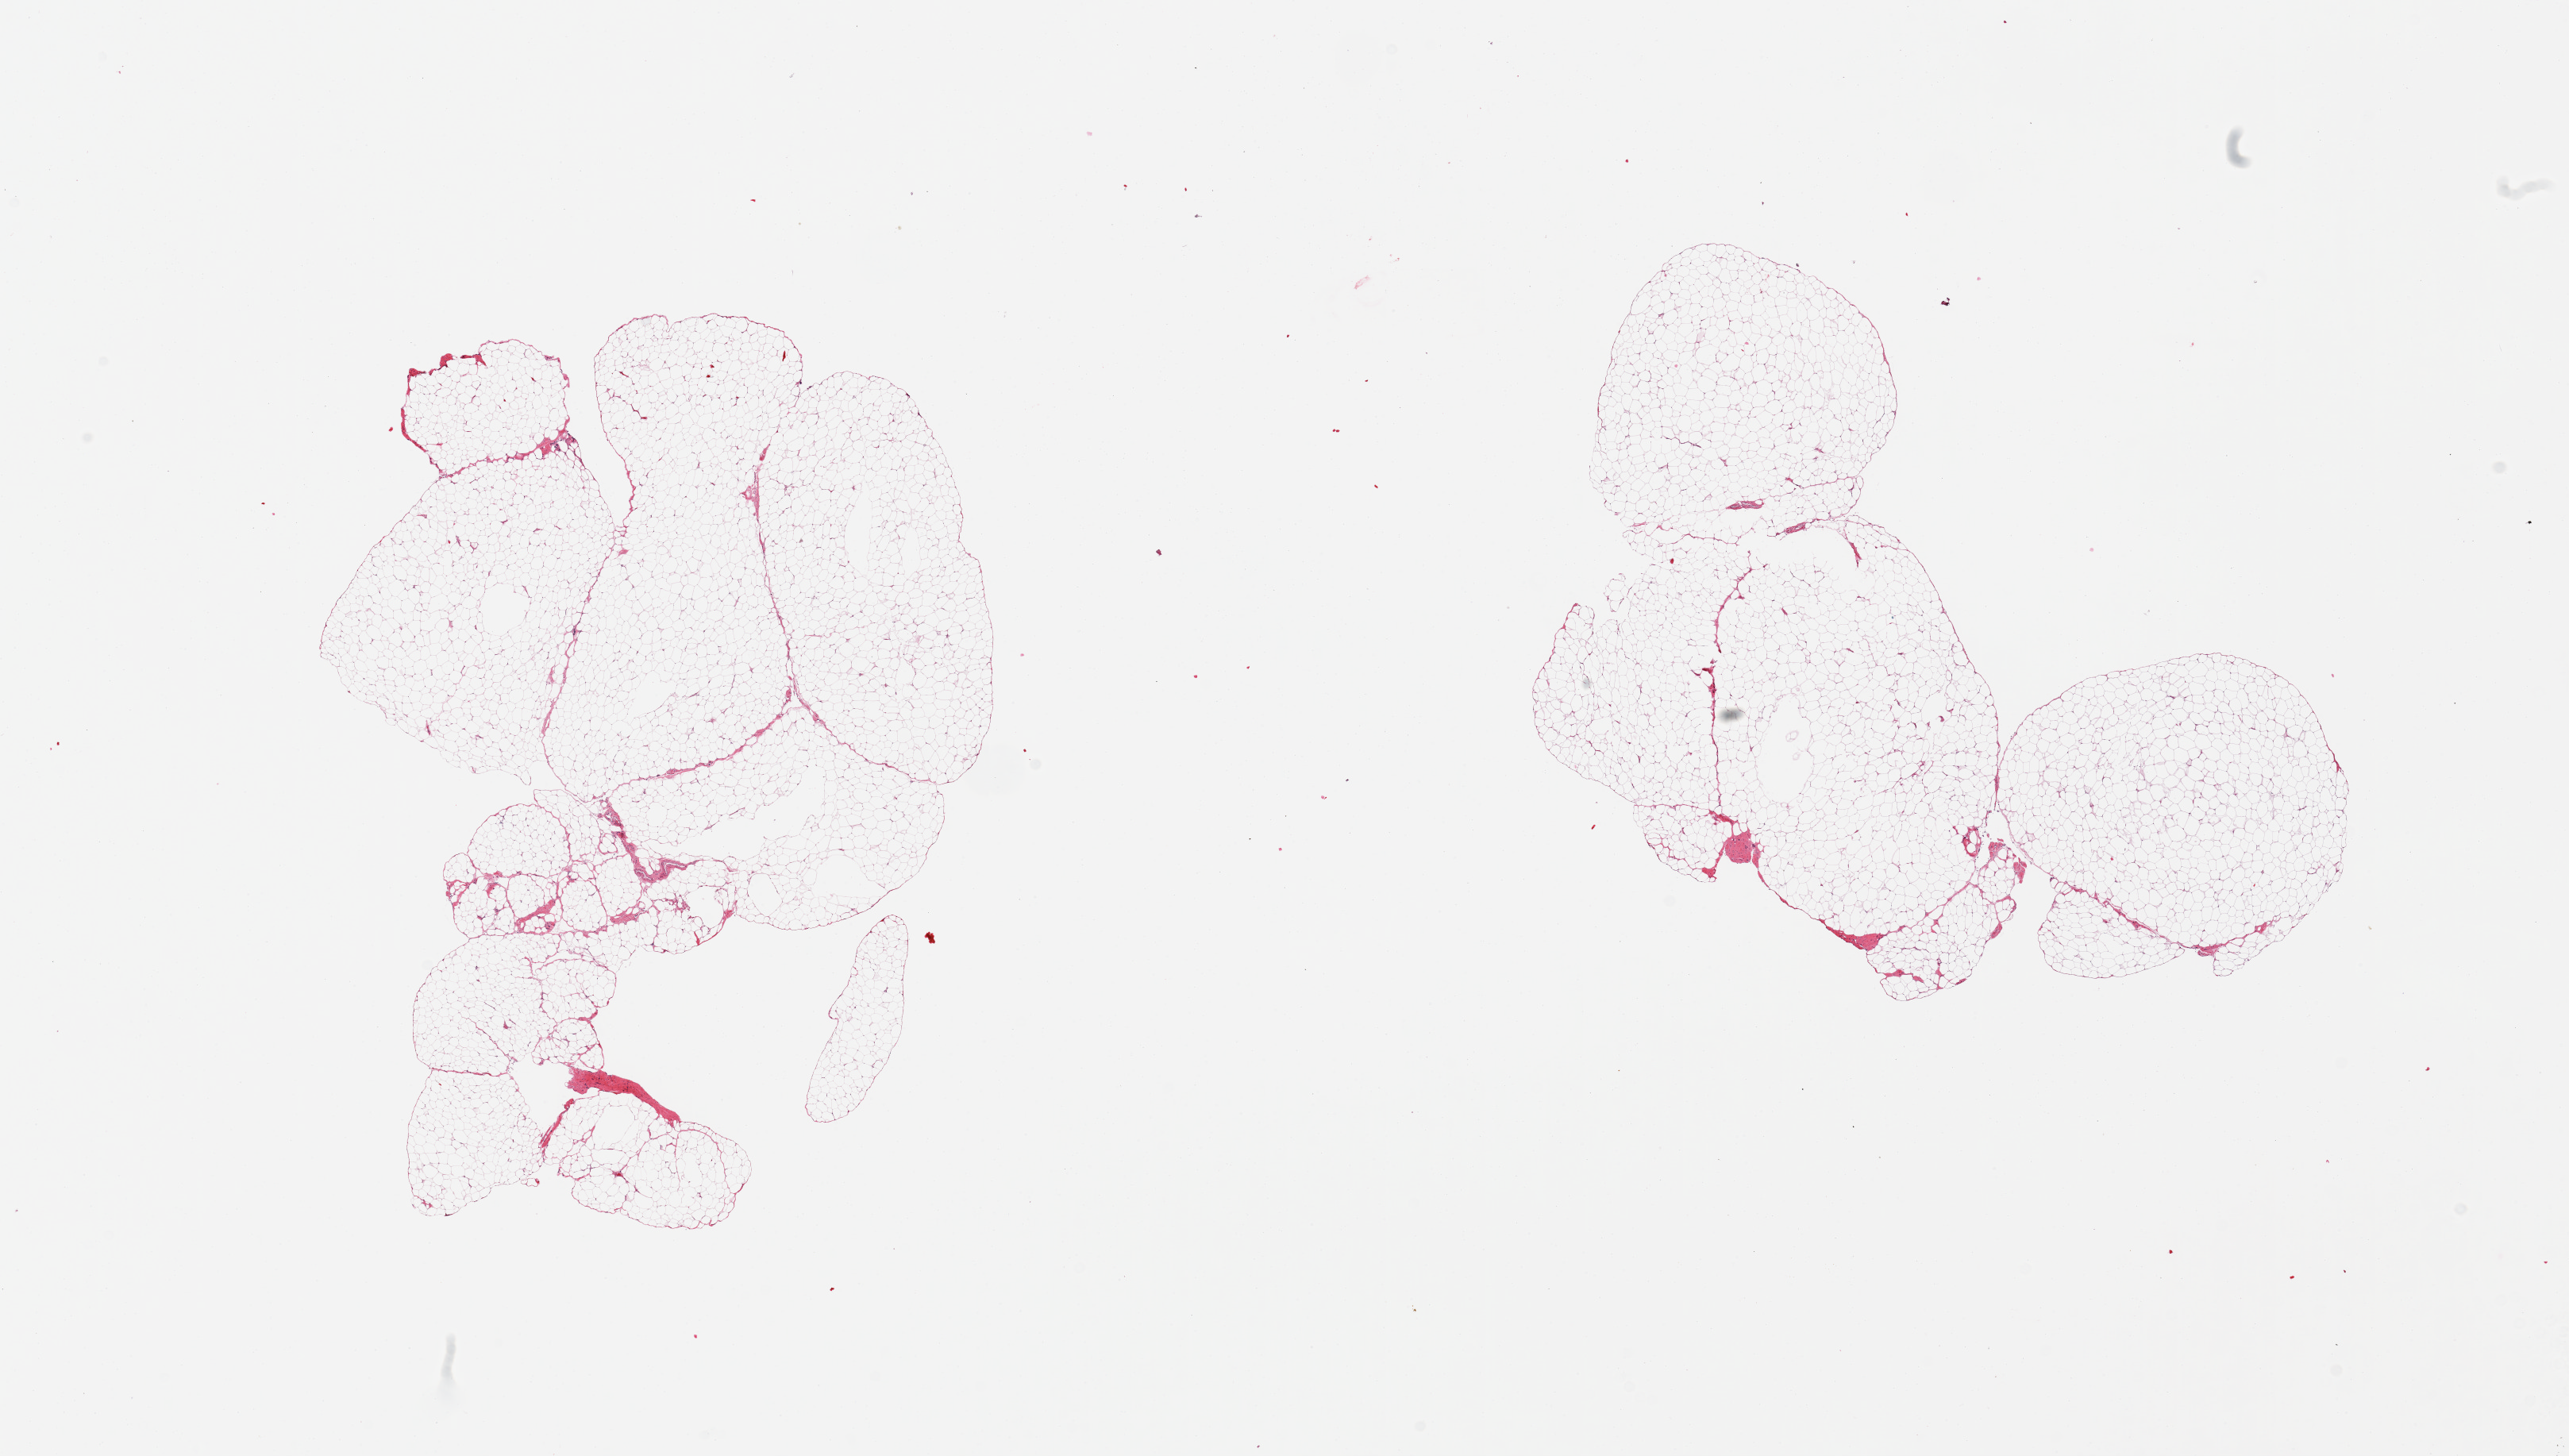
Digitized H&E-stained section, brightfield, shown as a low-resolution overview of the whole scanned area (about 25.6 x 14.5 mm, from a 20x scan). PAXgene-fixed, paraffin-embedded tissue. Sampled site (target tissue): omentum. Tissue donor sample.
• review note (as recorded): 2 pieces